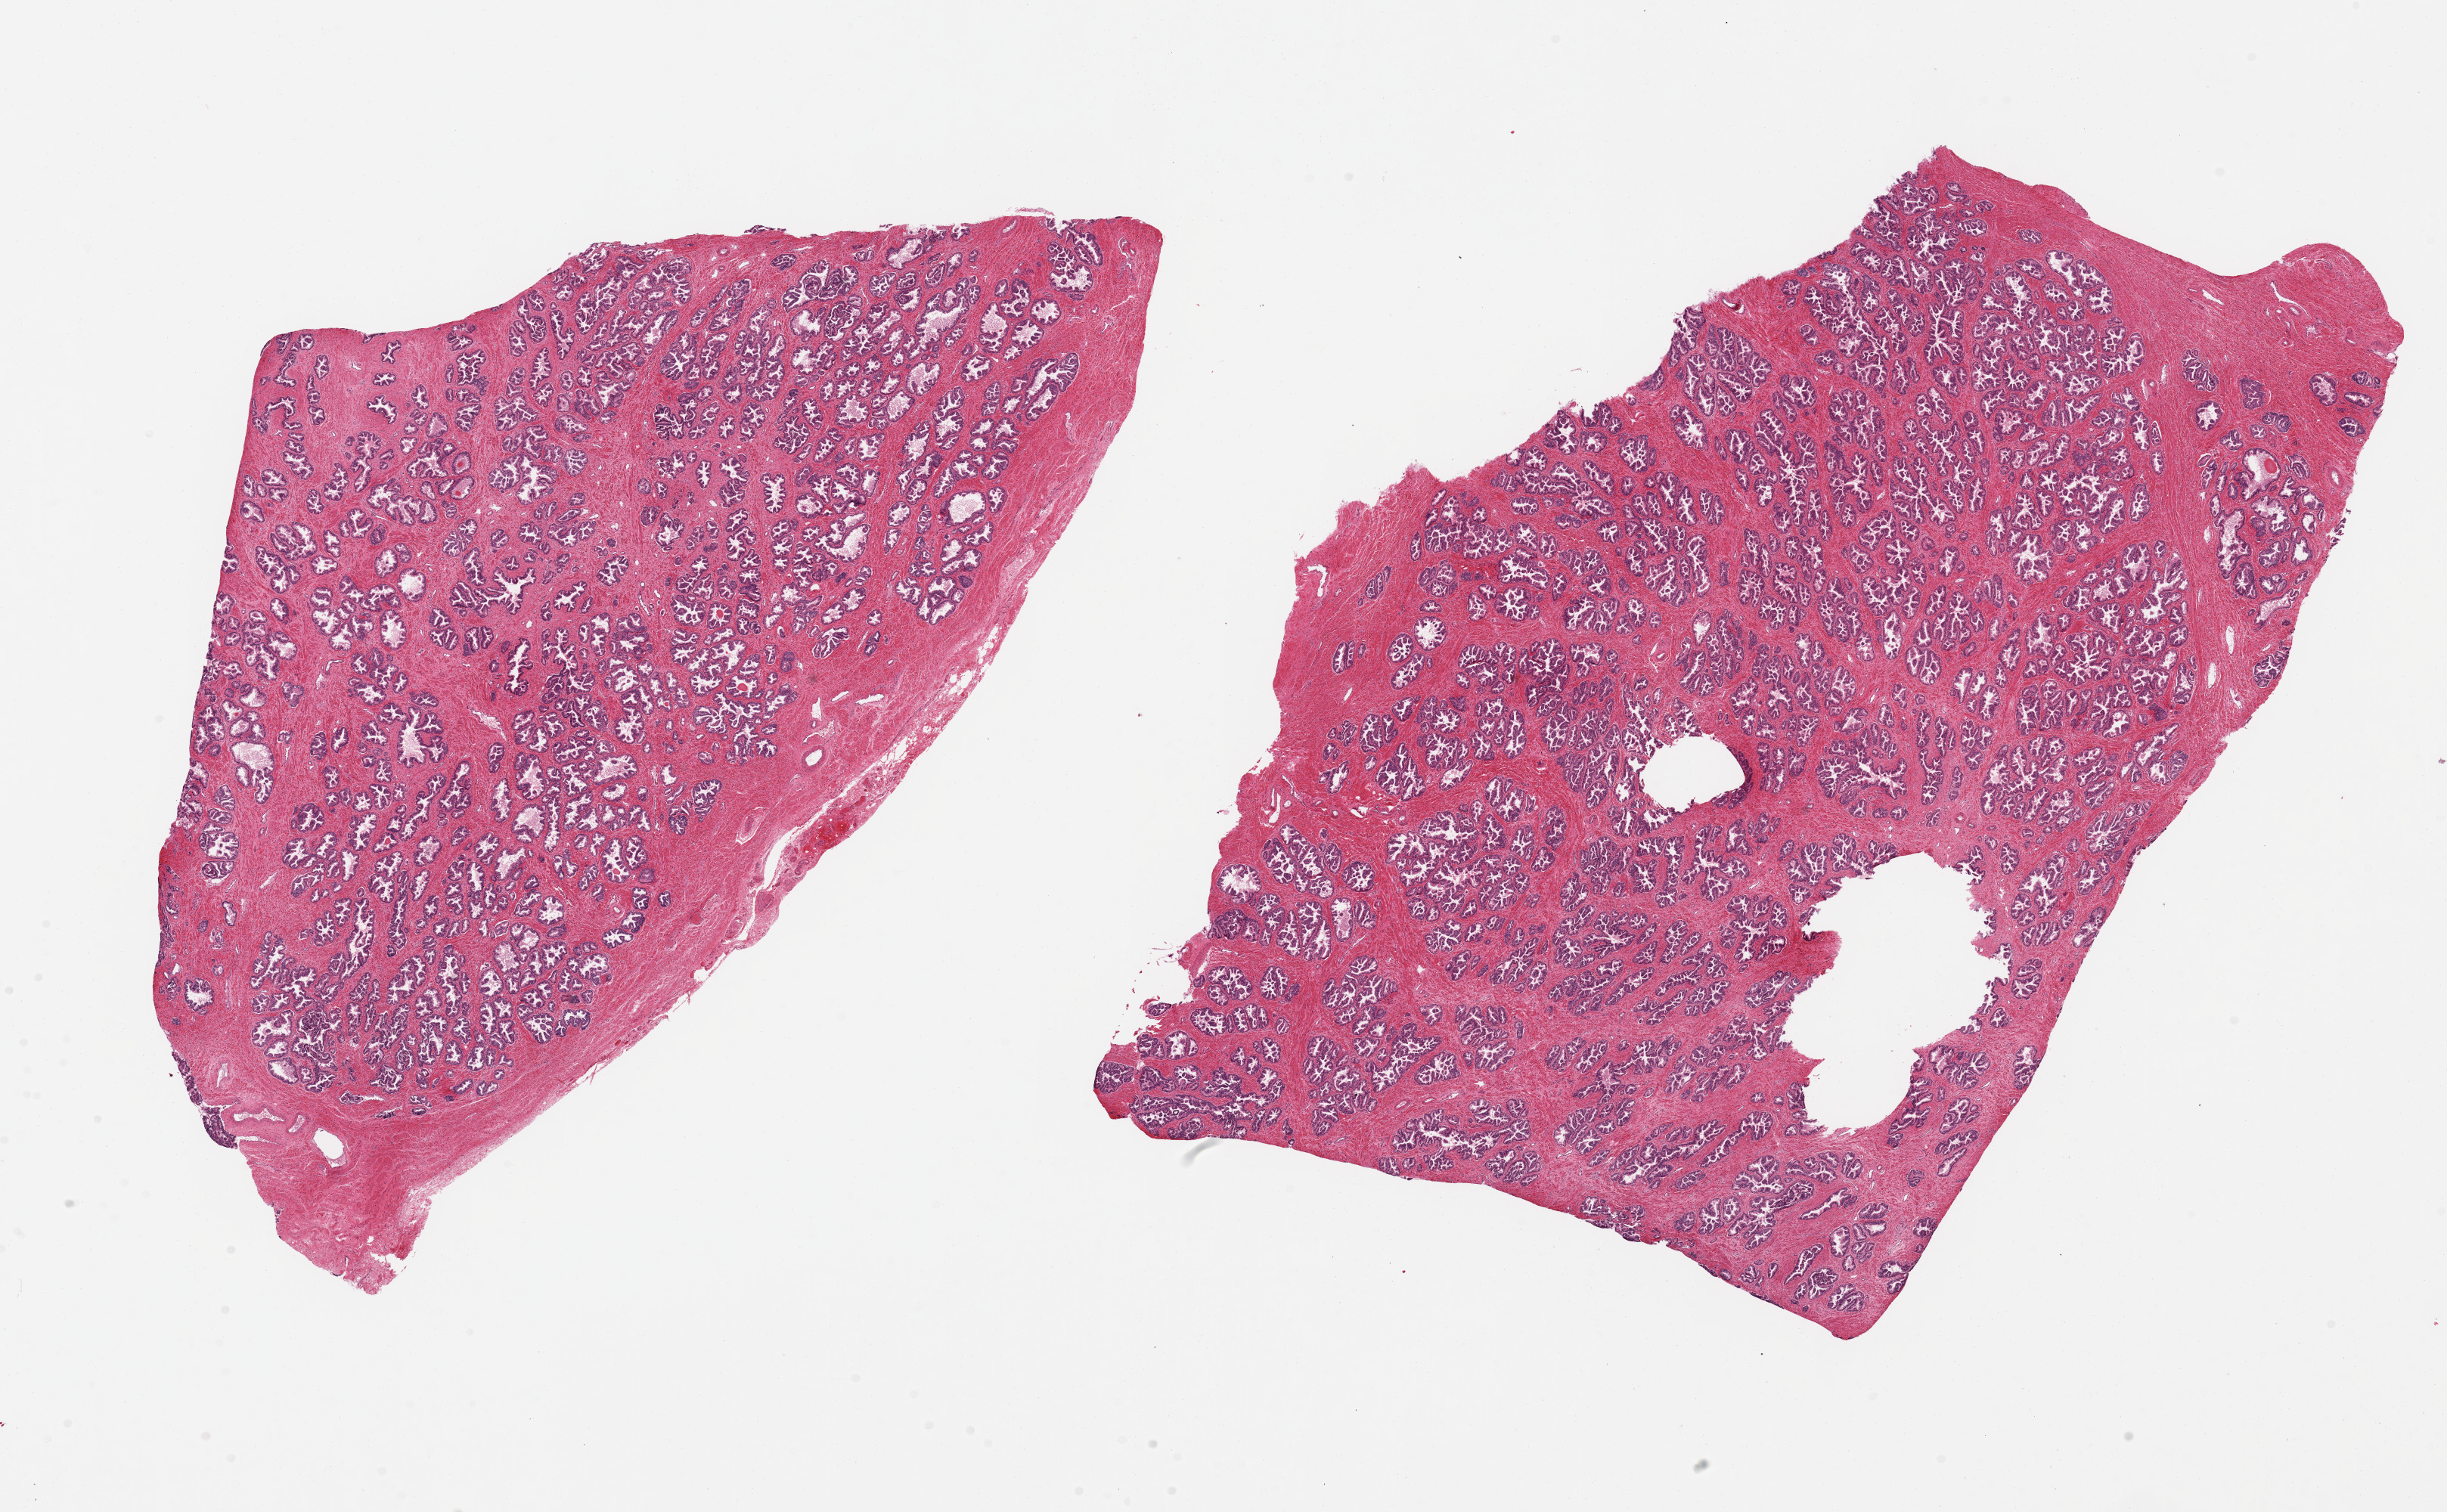
Whole-slide image, H&E stain, whole scanned area (about 25.6 x 15.8 mm, acquisition: 20x scan) shown as a low-resolution overview. PAXgene-fixed, paraffin-embedded tissue. Target tissue: prostate. Tissue donor sample. Donor: male.
Pathologist's review note for this sample: 2 pieces; admixture of glands and stroma.